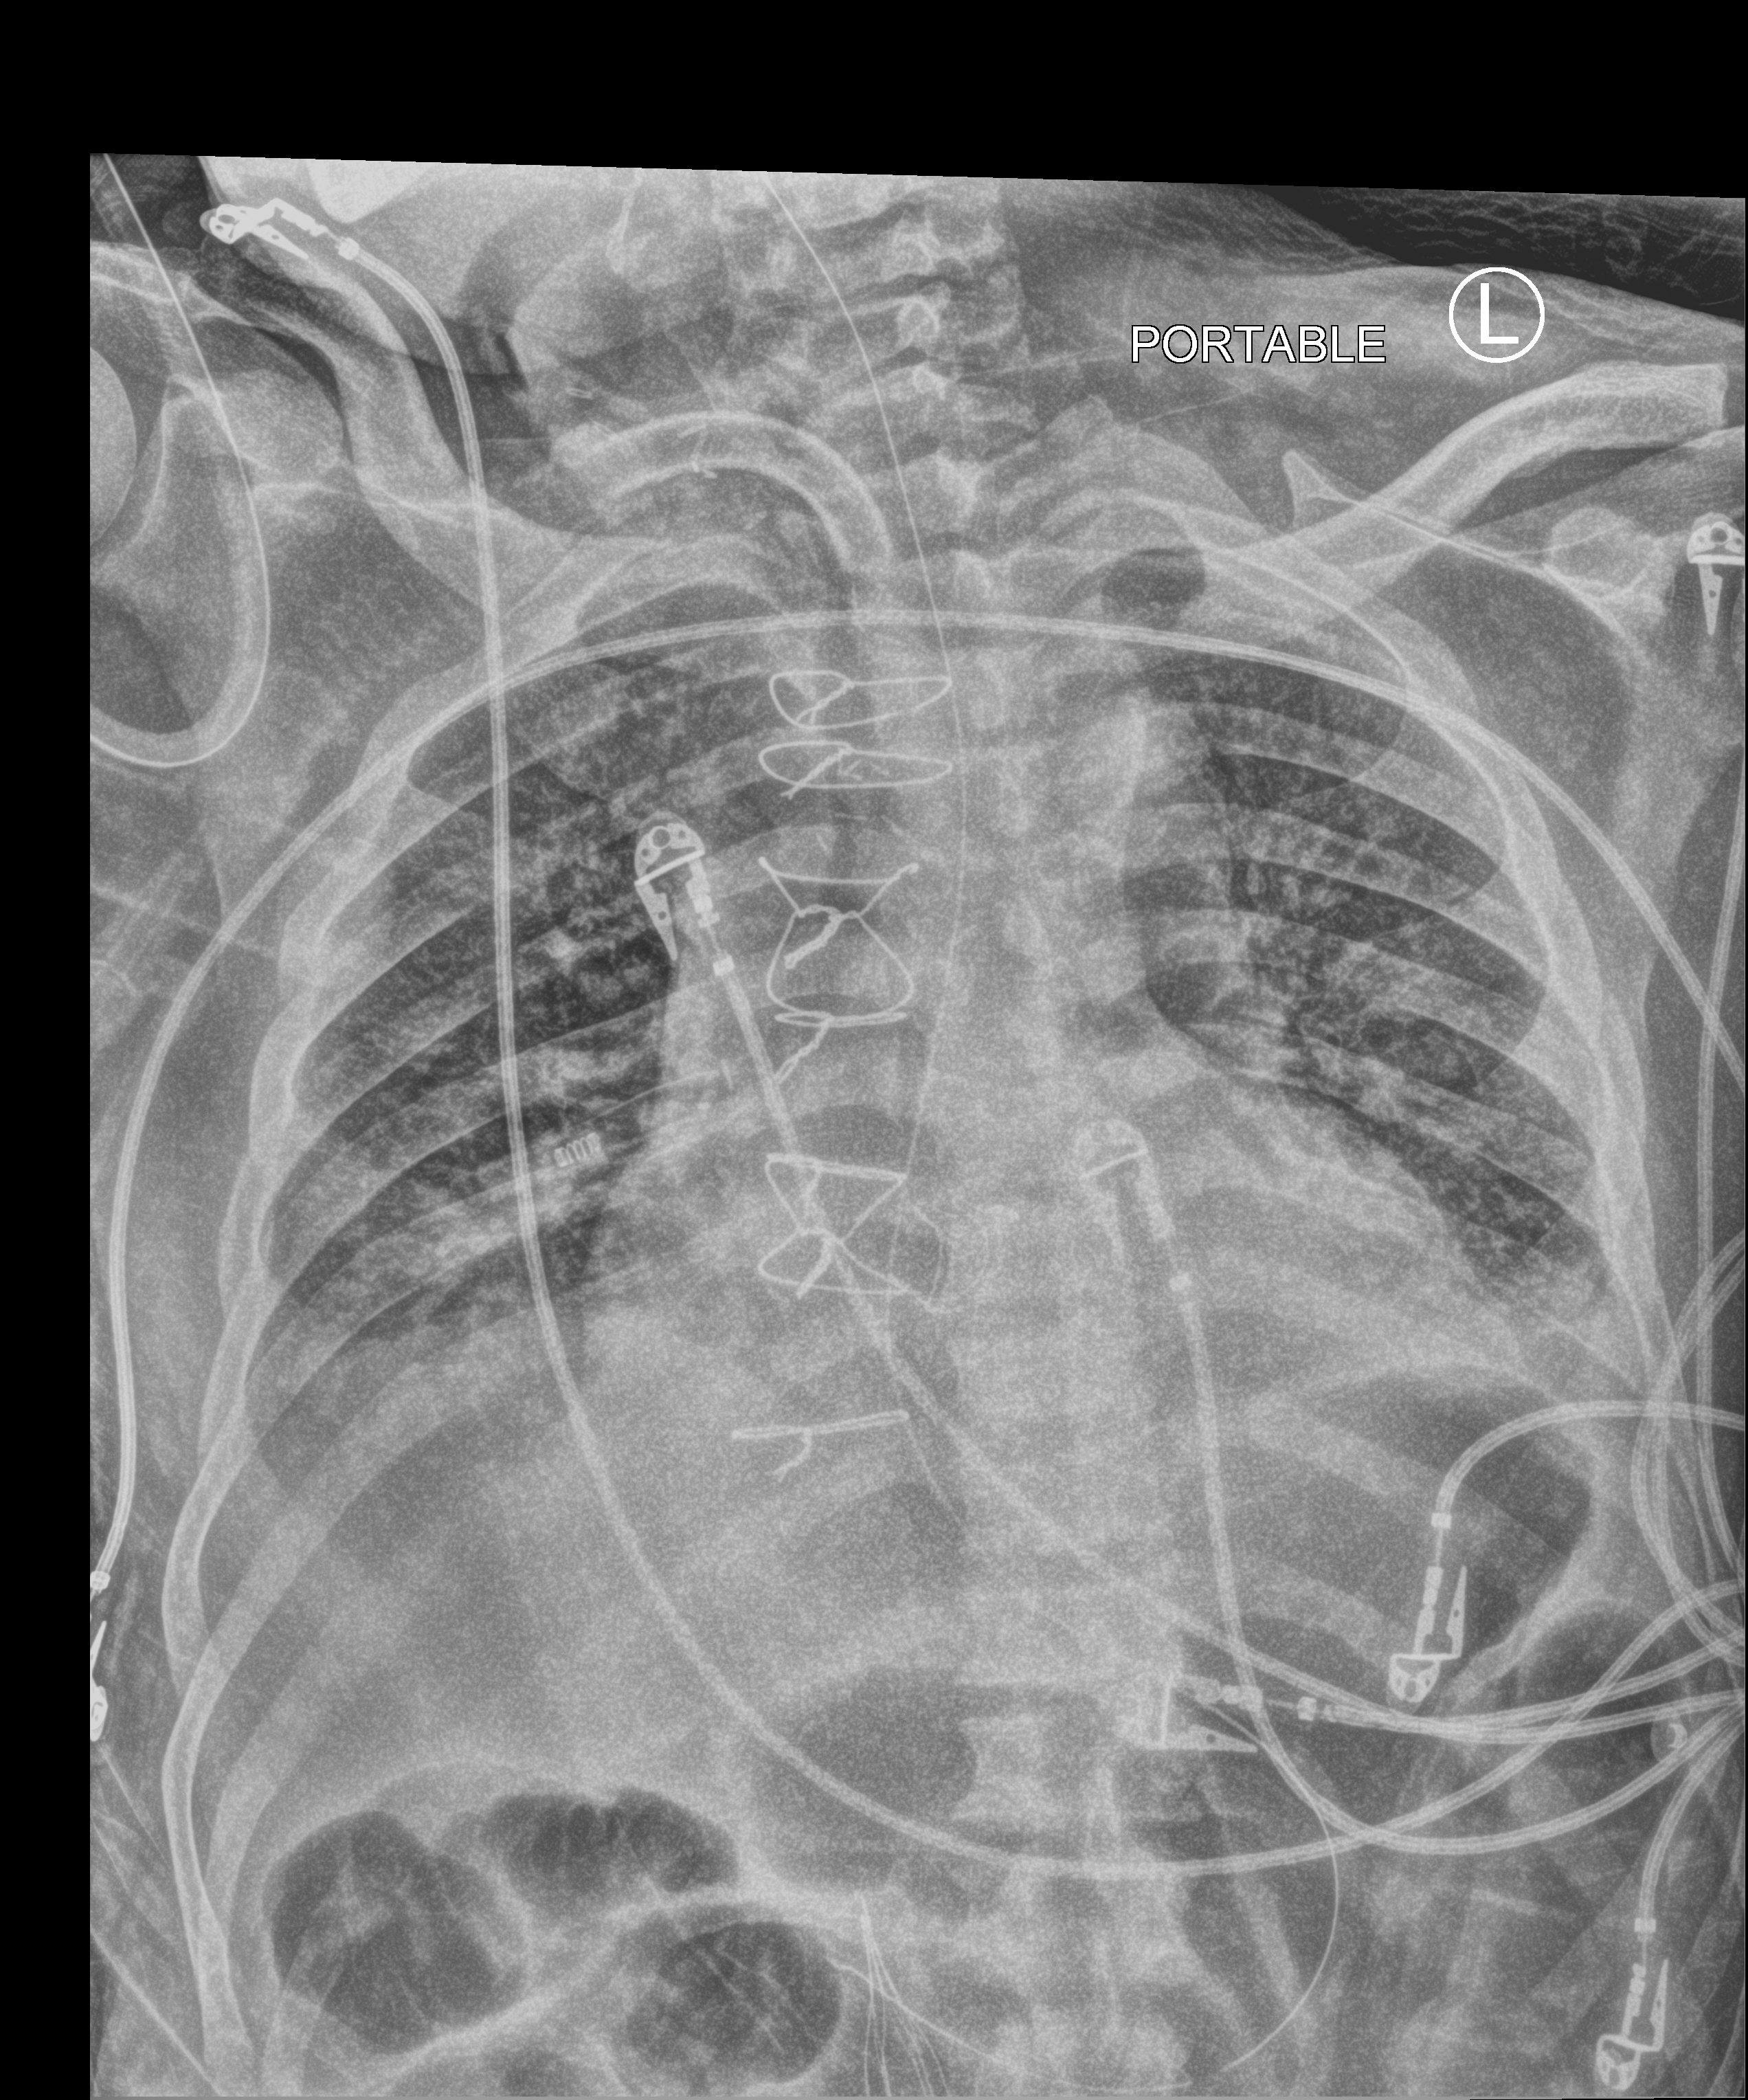
Portable chest radiograph; anteroposterior (AP) projection. Patient hospitalised with COVID-19; male, aged 60–74 years.
Admission-level facts for this patient (not findings on this image; timing relative to this image not recorded):
- diabetes (admission record): no
- admitted to intensive care during this hospital stay: yes